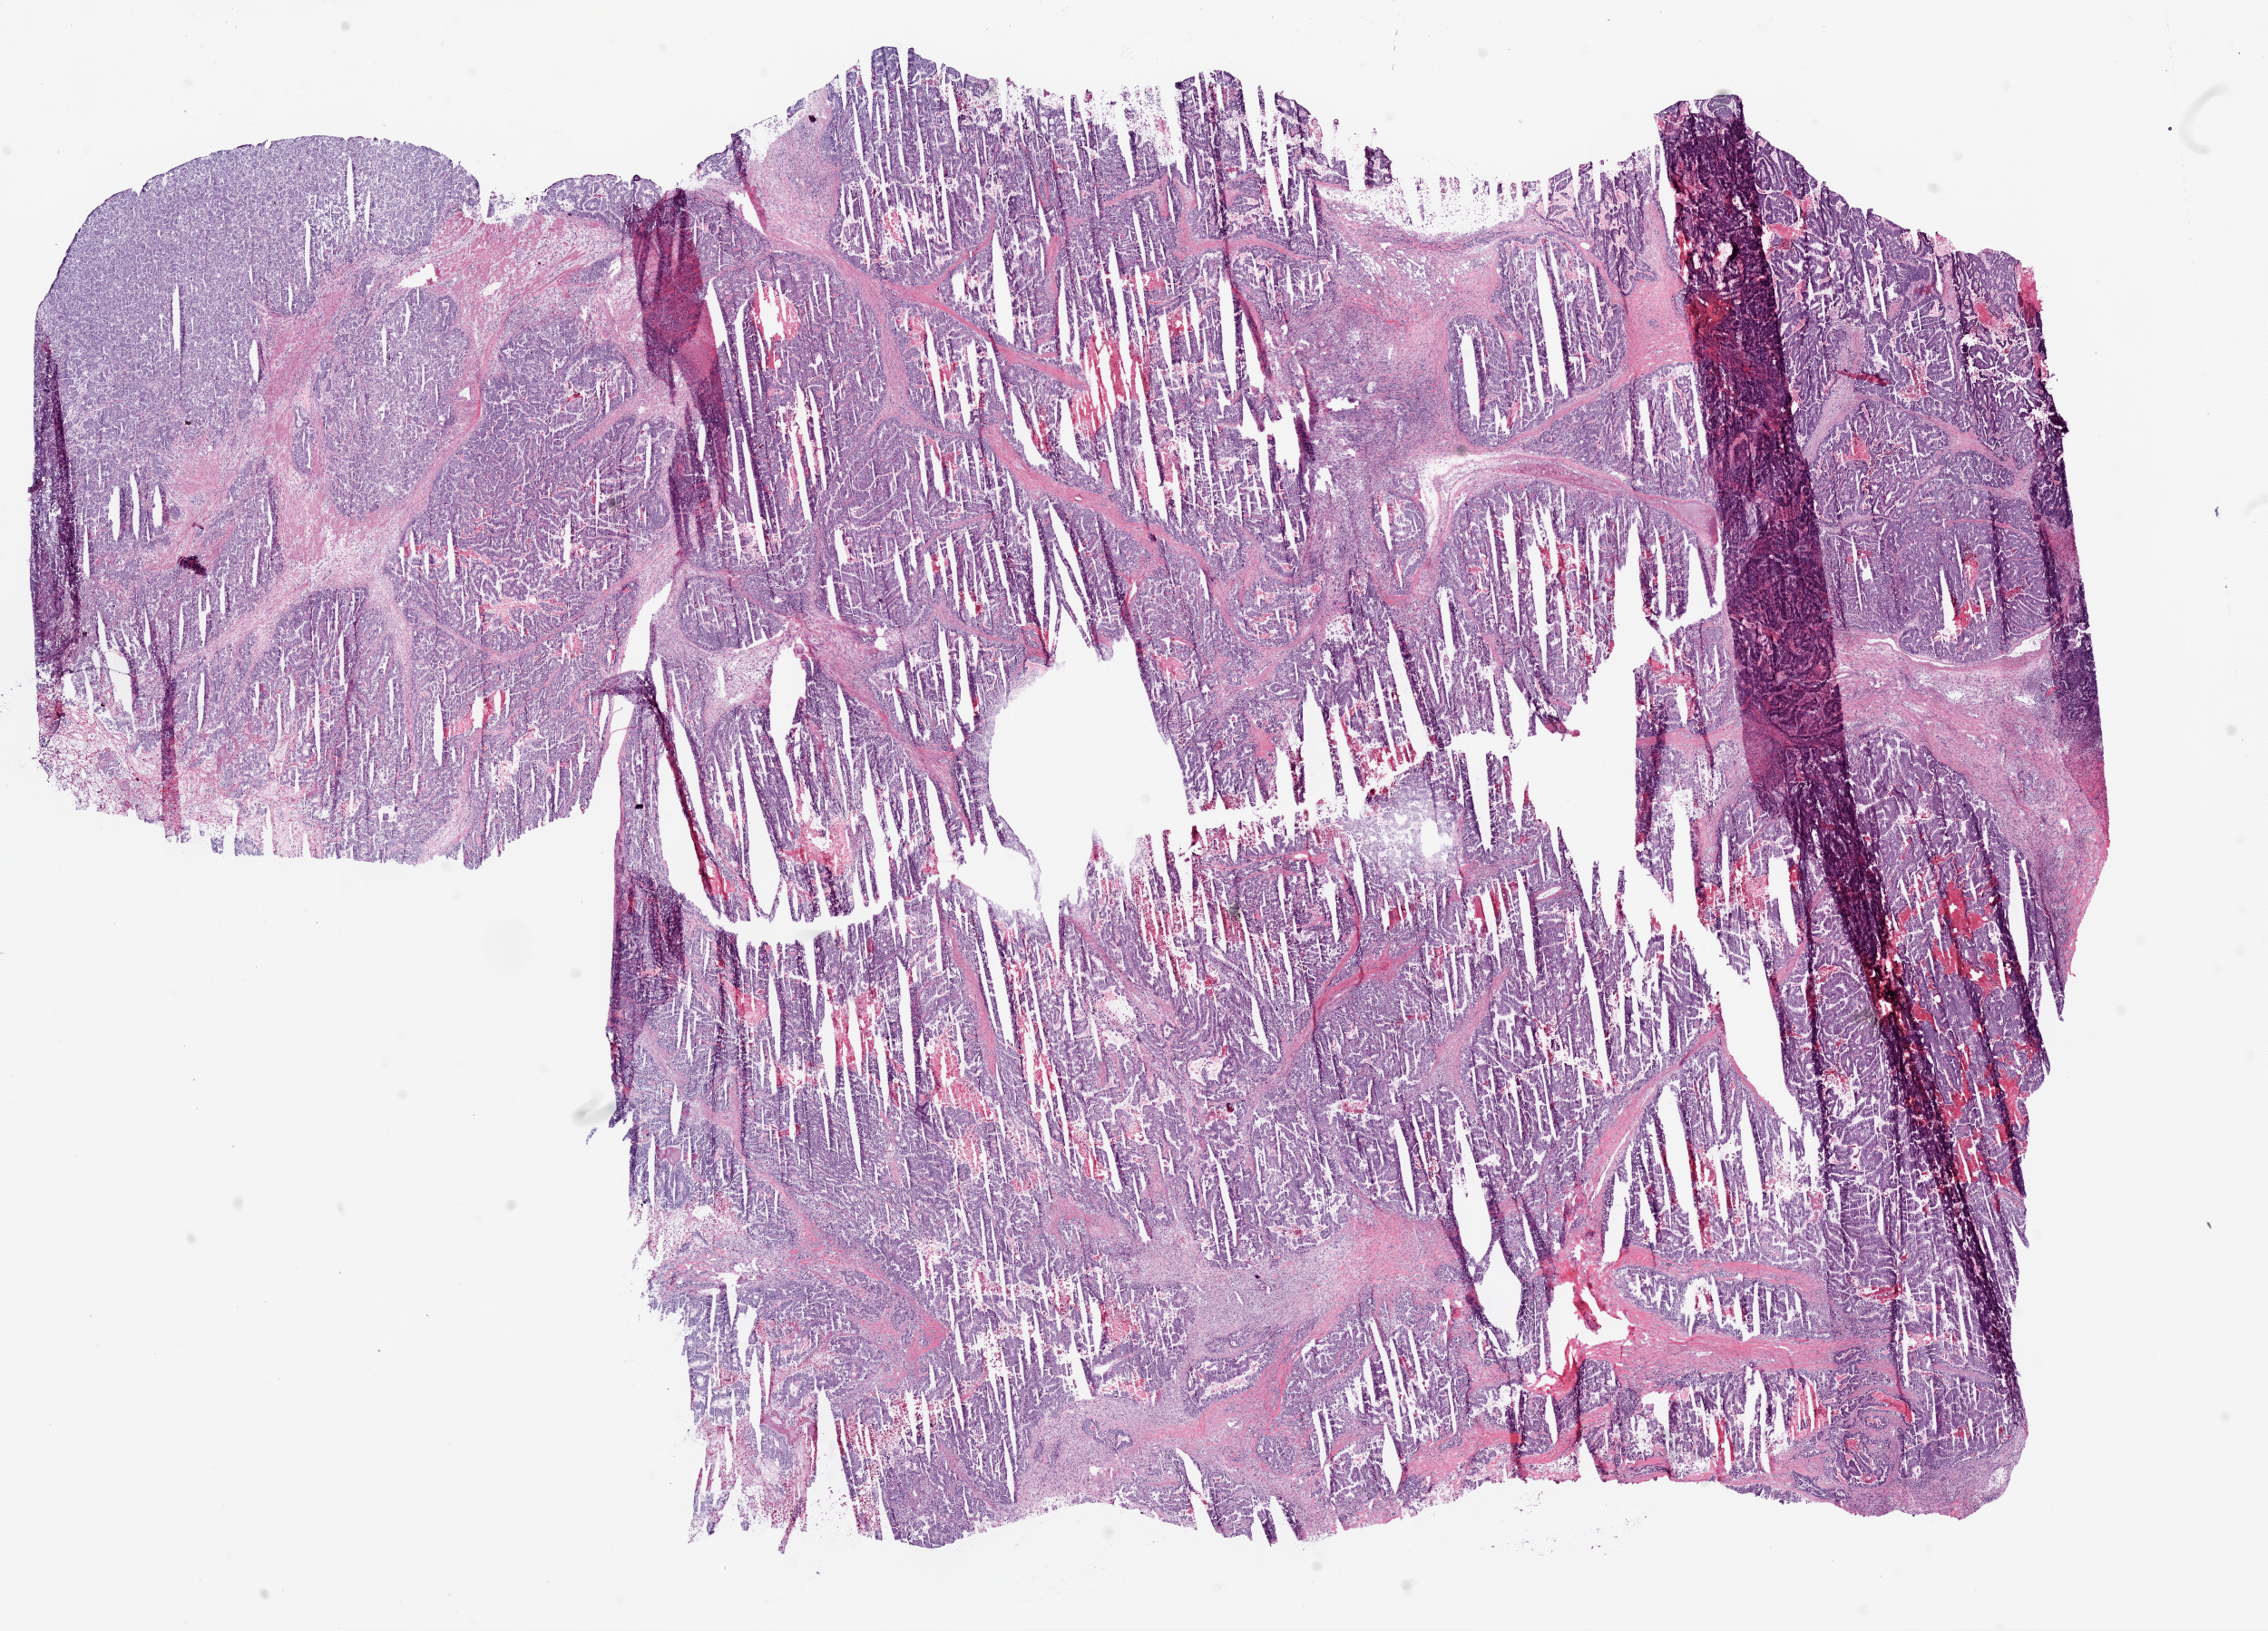
H&E whole-slide image, low-resolution overview of the scanned area, about 20.1 x 14.4 mm (acquisition: 20x scan); frozen section; sample: primary tumour, stomach. Male patient; age at initial diagnosis 87 years. Histologic grade: G2 (moderately differentiated). Pathologist review of this section (percent, as recorded): tumour cells 80%, tumour nuclei 80%, normal cells 0%, stromal cells 10%, necrosis 10%.
- histologic diagnosis: Adenocarcinoma, NOS